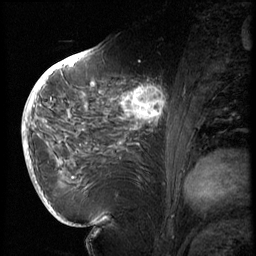
Breast MRI (dynamic contrast-enhanced), one sagittal slice; slice 31 of 72 in the series (ordered by position); 3 images stored at this slice position (order not interpretable as contrast timing); 1.5 T; TE 4.2 ms, TR 8.9 ms; 2.5 mm slice thickness; 256 × 256 image matrix, field of view 200 × 200 mm. Female patient, age 56 years. From the clinical record (not read from this slice): setting: breast cancer imaged before/during neoadjuvant chemotherapy.
Annotated regions visible in this slice (semi-automatic segmentation, software-assisted and operator-edited):
- analysis volume of interest (the breast-tissue region the enhancement analysis was run in; not a lesion): bounding box <114,76,177,138> (left, top, right, bottom; pixels)
- tumour enhancement mask (voxels above the 140 % enhancement threshold inside the analysis volume of interest): <121,85,168,124>